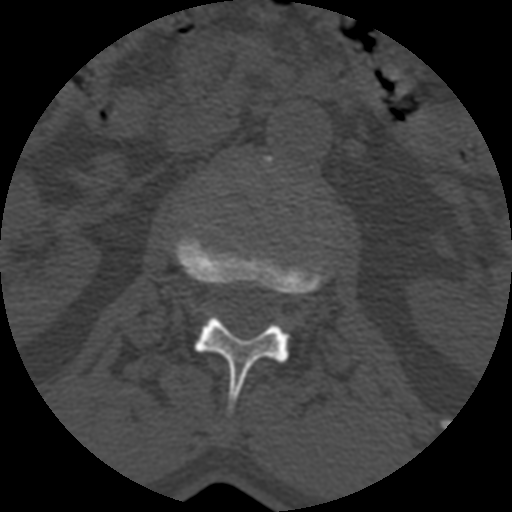
CT including the spine, one axial slice. Position 354 of 399 along the scan axis. Reconstruction kernel STANDARD. Bone window (W 1800 / L 400 HU). 512 × 512 image matrix, field of view 160 × 160 mm. Patient age 71 years. From the clinical record (not read from this slice): primary cancer: prostate.
Outlined on this slice (semi-automatic segmentation, software-assisted and operator-edited):
- L1 vertebra: box from (x=172, y=235) to (x=330, y=410) px
- L2 vertebra: (x=264, y=158)–(x=271, y=164)